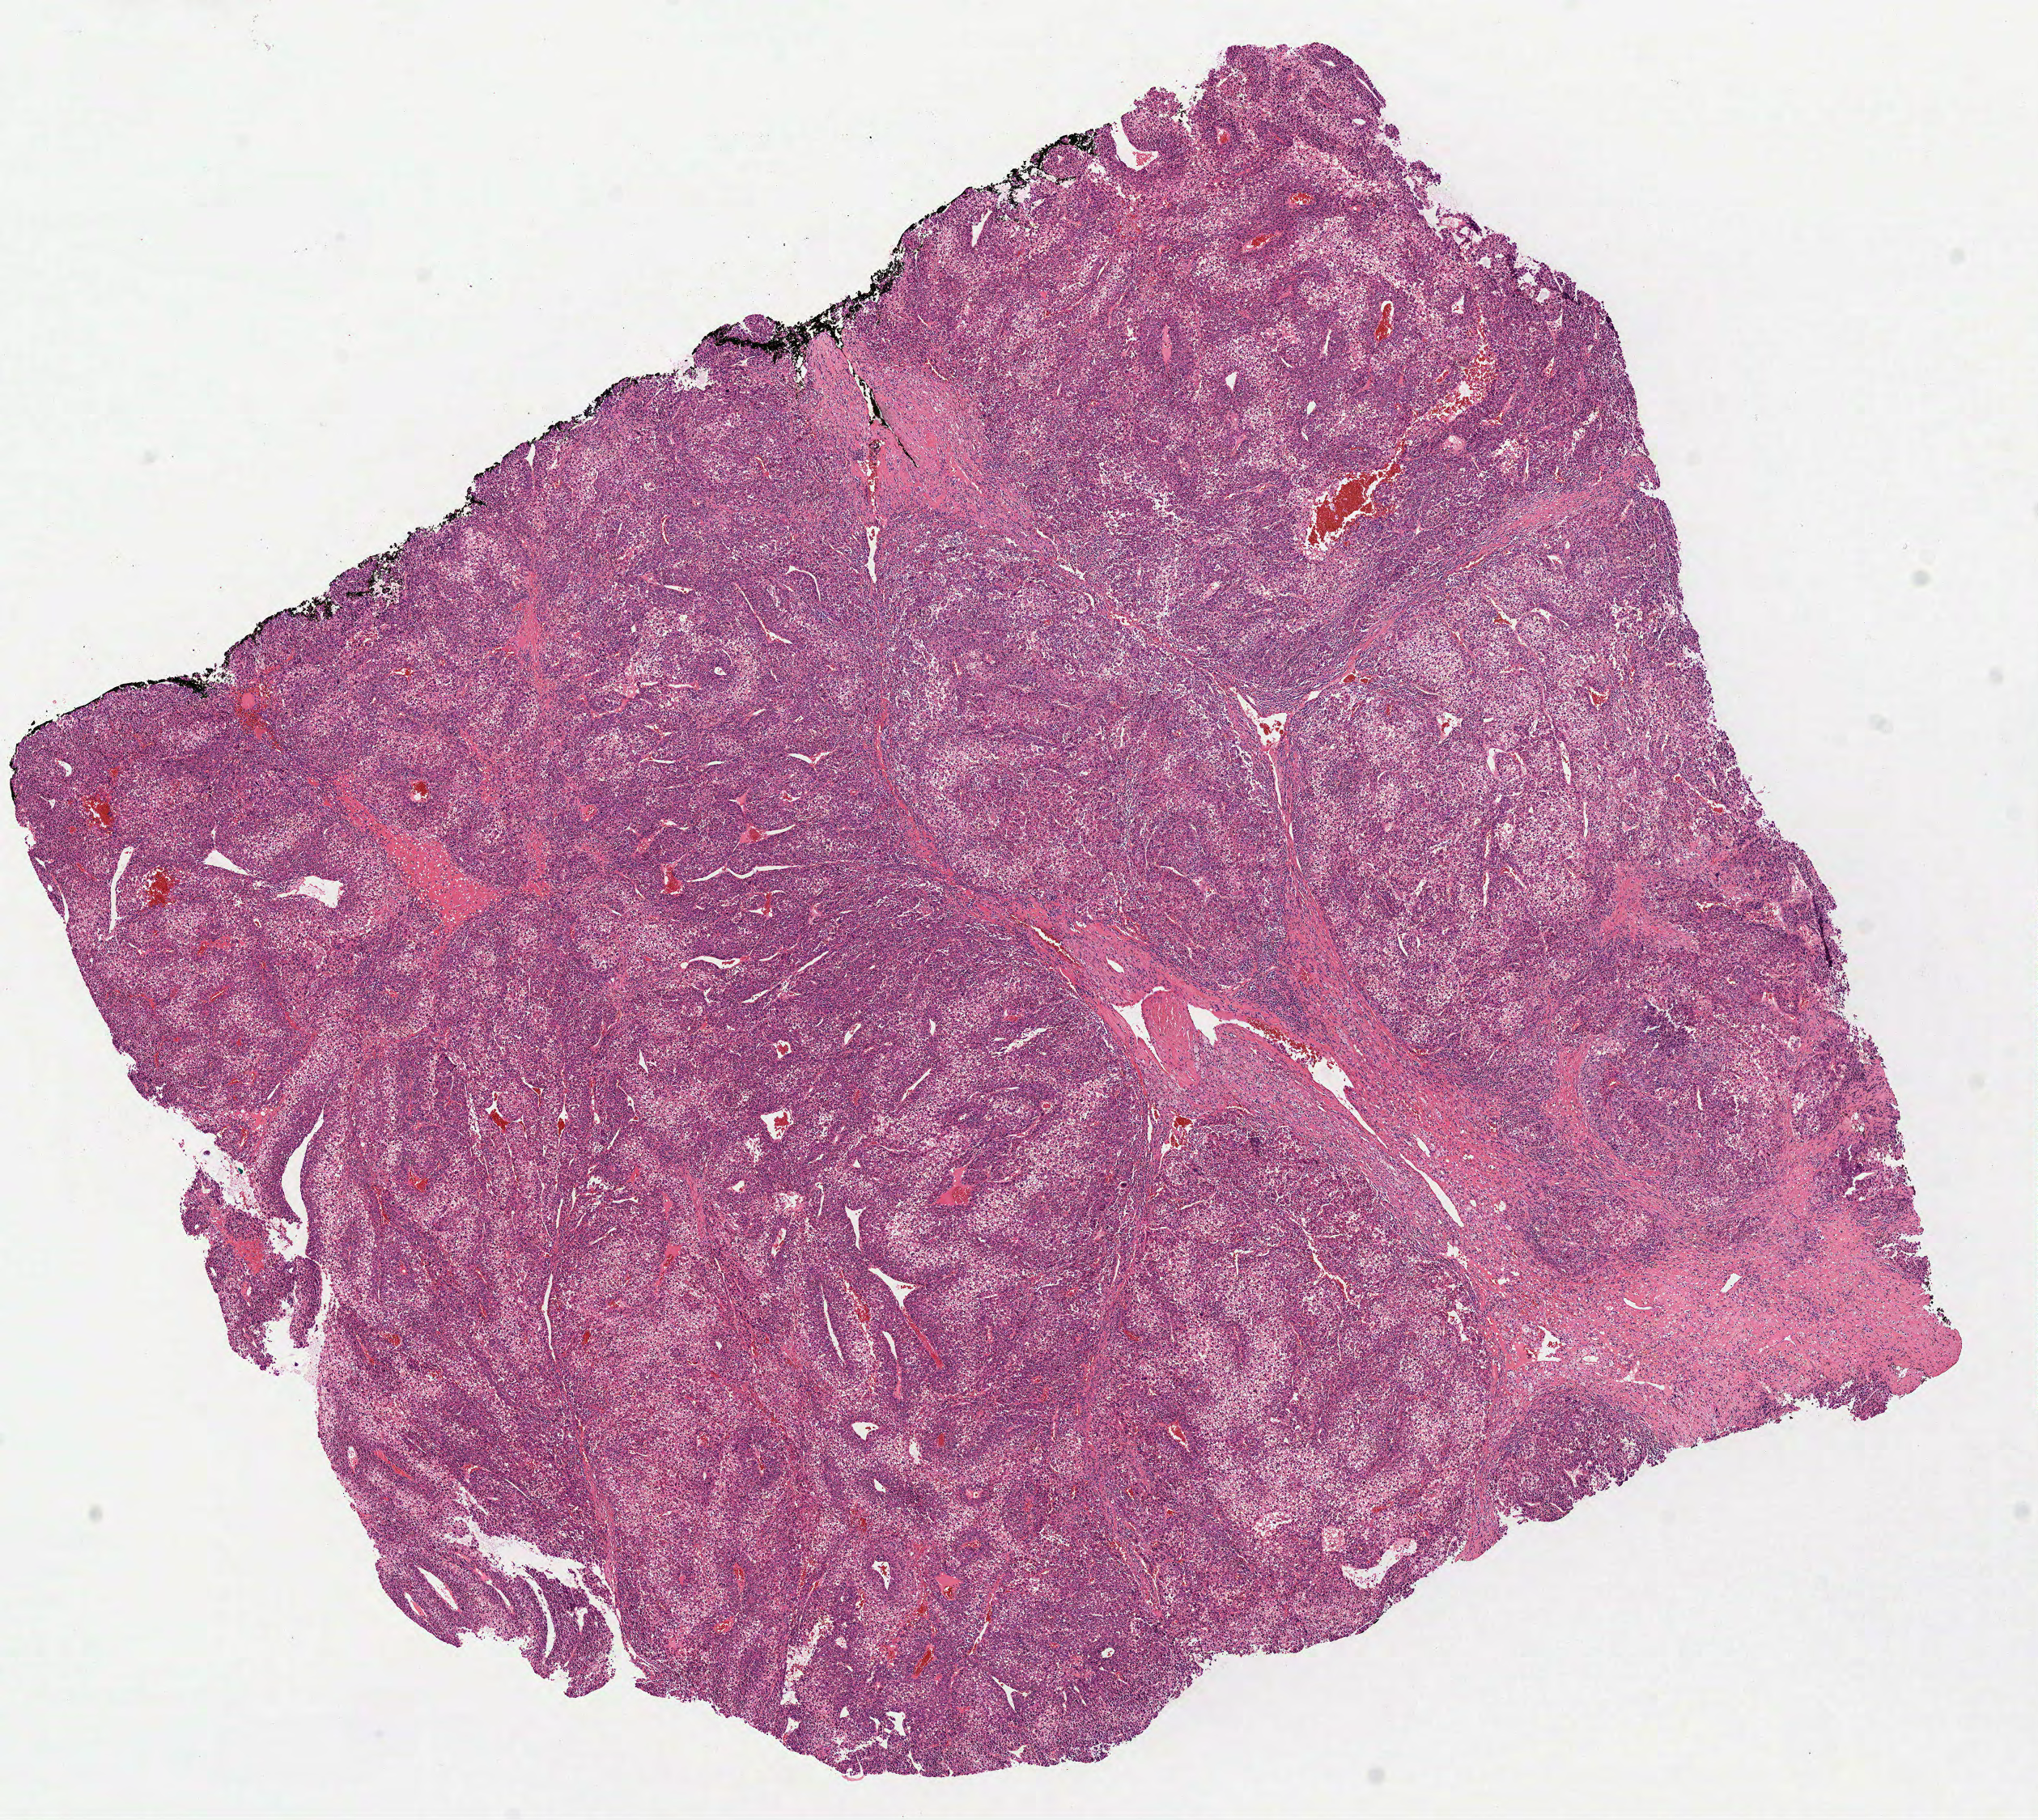
Digitized H&E-stained tissue section (whole slide), low-resolution overview of the scanned area, about 10.2 x 9.1 mm; formalin-fixed paraffin-embedded (FFPE) diagnostic section; sample: primary tumour, liver. Male, age 52 years at initial diagnosis. Histologic grade: G2 (moderately differentiated).
• histologic diagnosis: Hepatocellular carcinoma, NOS
• AJCC pathologic stage: I (7th edition)